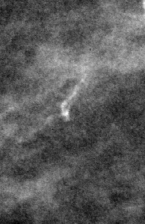
Cropped region of a digitized screen-film mammogram centred on a radiologist-marked abnormality; right breast; MLO view.
Calcifications, morphology fine linear branching; BI-RADS assessment category 2; benign without callback (not worked up further).